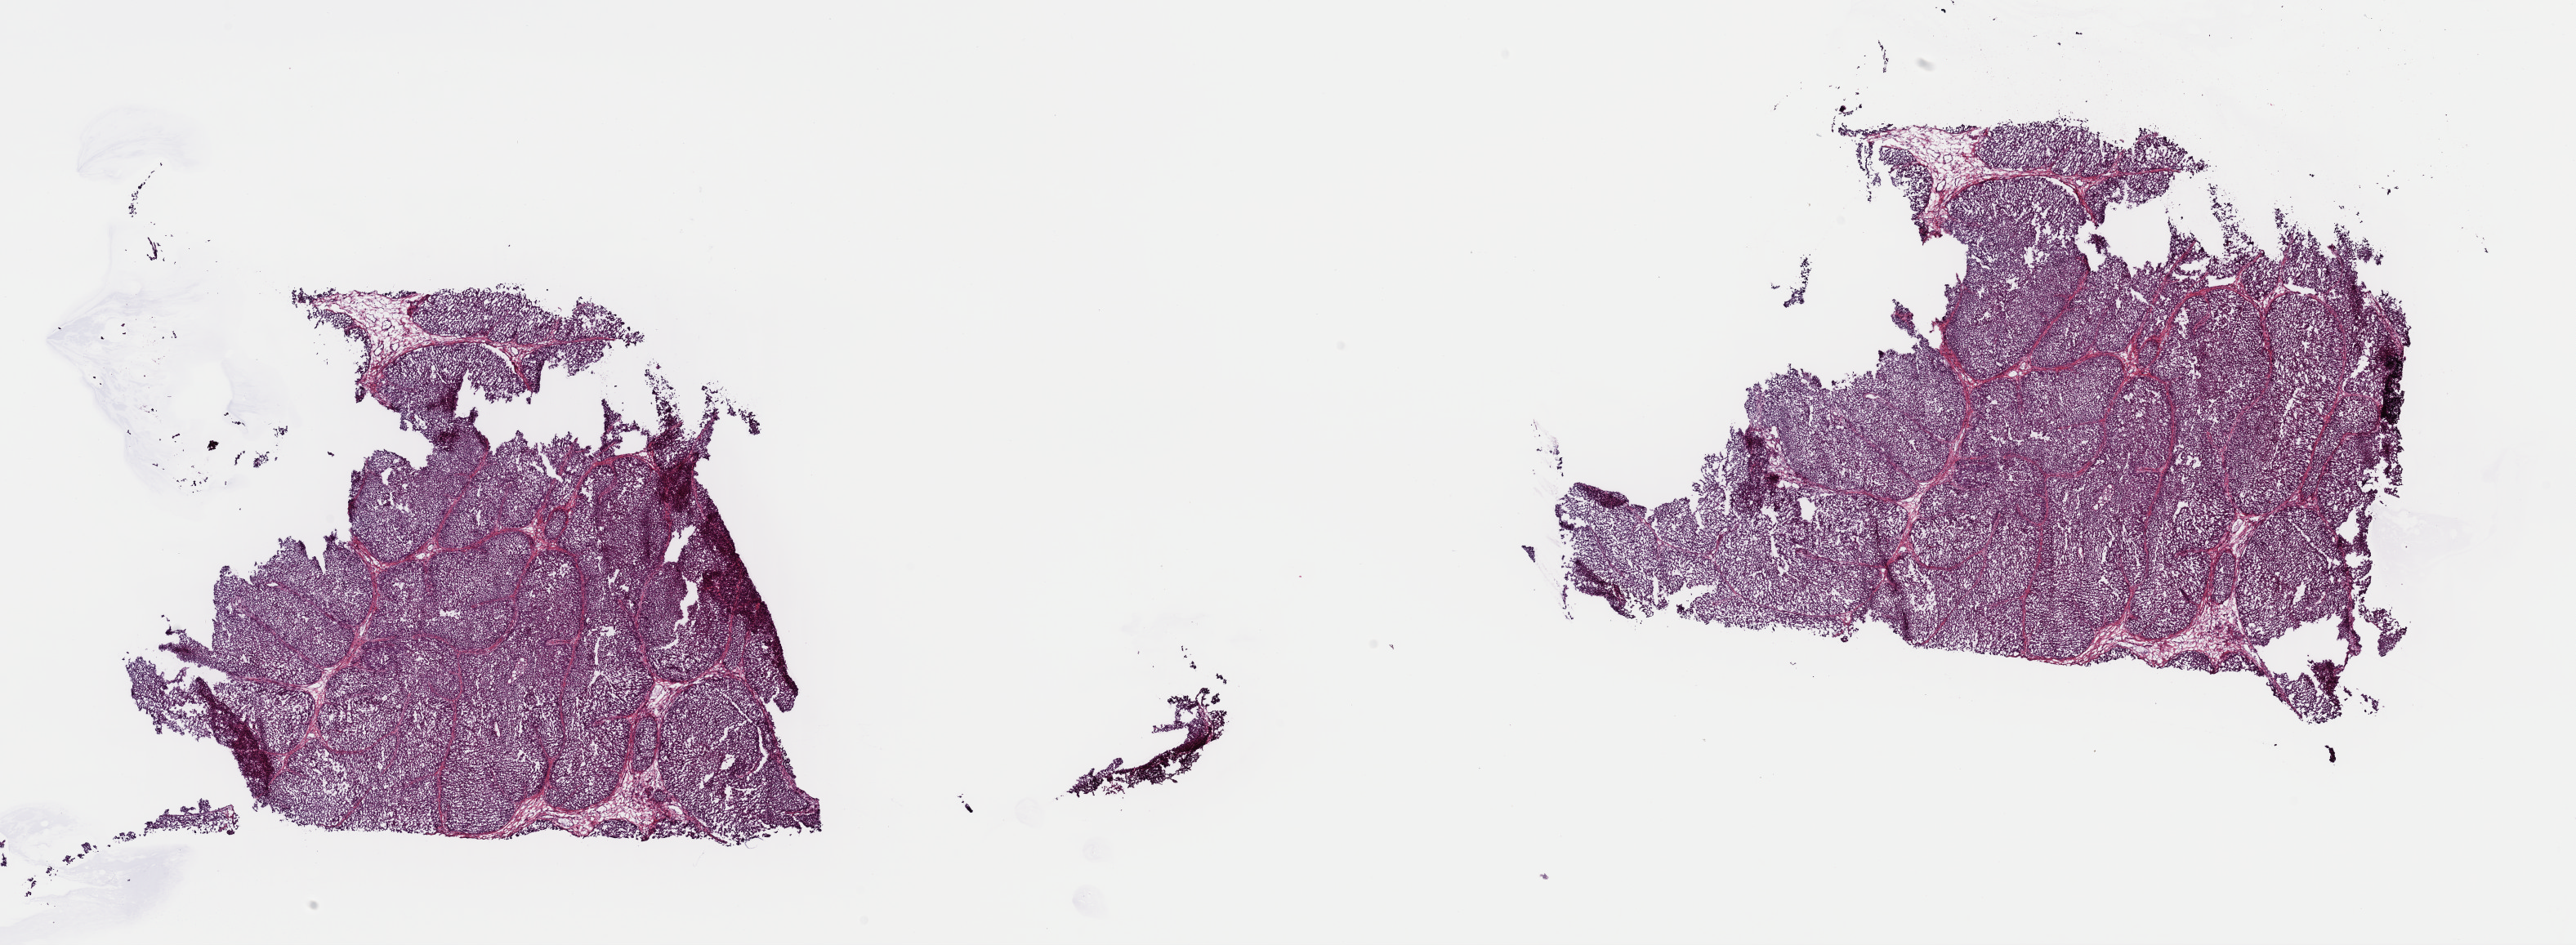
Digitized H&E tissue section (whole slide) — low-resolution overview of the scanned area, about 24.9 x 9.1 mm, frozen section from the top of the tissue portion, primary tumour sample from the bladder. Male, age 67 years at initial diagnosis. Histologic grade: low grade. Composition of this section per pathologist review: tumour cells 90%, tumour nuclei 95%, normal cells 0%, stromal cells 10%, necrosis 0%. Infiltration values recorded for this section: lymphocyte infiltration 0%, monocyte infiltration 0%, neutrophil infiltration 0%.
- histologic diagnosis: Transitional cell carcinoma
- AJCC pathologic stage: II (6th edition)